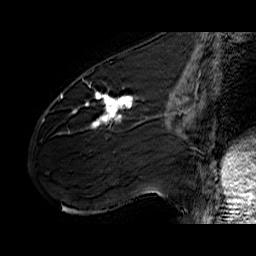
Breast MRI (dynamic contrast-enhanced), one sagittal slice; position 25 of 60 along the scan axis; dynamic contrast-enhanced series, time point 2 of 6 at this slice position (early post-contrast); 1.5 T; TE 6.4 ms, TR 32.9 ms; 256 × 256 image matrix, field of view 200 × 200 mm. Female patient. From the clinical record (not read from this slice): setting: breast cancer imaged before/during neoadjuvant chemotherapy; receptor status: HER2-positive.
Outlined on this slice (semi-automatic segmentation, software-assisted and operator-edited):
- analysis volume of interest (the breast-tissue region the enhancement analysis was run in; not a lesion): bounding box <61,77,141,142> (left, top, right, bottom; pixels)
- tumour enhancement mask (voxels above the 100 % enhancement threshold inside the analysis volume of interest): <61,92,137,127>